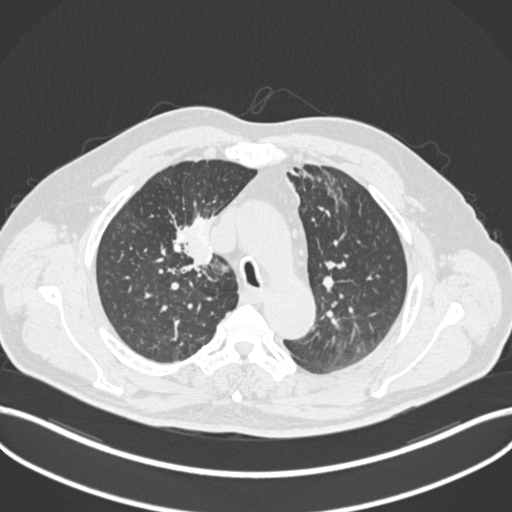
Chest CT, one axial slice. Slice 143 of 255 in the series (ordered by position). Reconstruction kernel B30f. 120 kVp. Lung window (W 1500 / L -600 HU). 1 mm slice thickness. 512 × 512 image matrix, field of view 400 × 400 mm. Patient: male, 60 years. From the clinical record (not read from this slice): clinical TNM (as recorded): T1b N1 M0.
Annotated regions visible in this slice (rectangle marked by the reading radiologist):
- lung tumour (recorded histology: squamous cell carcinoma): bounding box <156,205,223,271> (left, top, right, bottom; pixels)